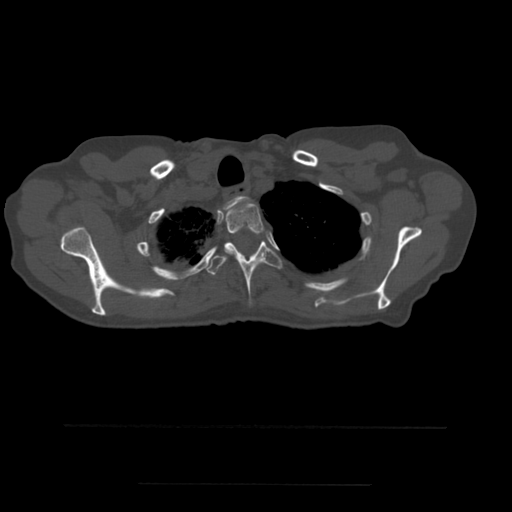
CT including the spine, one axial slice. Slice 428 of 544 in the series (ordered by position). Bone window (W 1800 / L 400 HU). 512 × 512 image matrix. Patient age 58 years. Case-level facts recorded for this patient, not image findings: primary cancer: lung.
Structures marked on this image (semi-automatically segmented with operator editing):
- T1 vertebra: bounding box (x1, y1, x2, y2) in pixels: (224, 196, 247, 211)
- T2 vertebra: (225, 202, 264, 255)
- T3 vertebra: (207, 241, 282, 304)